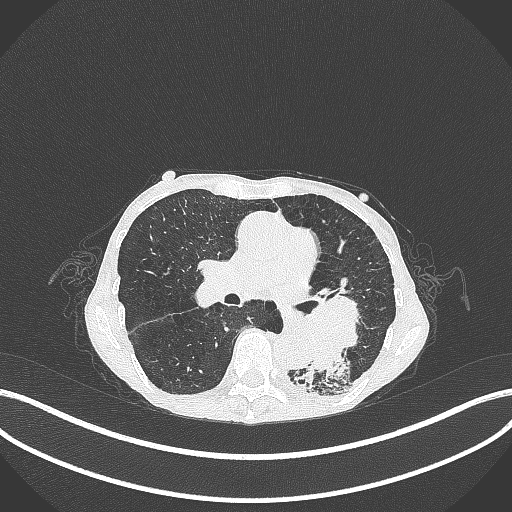
Chest CT, one axial slice; position 148 of 347 along the scan axis; reconstruction kernel B70f; 120 kVp; lung window (W 1500 / L -600 HU); 1 mm slice thickness; 512 × 512 image matrix, field of view 400 × 400 mm. Patient: female, 70 years. Case-level facts recorded for this patient, not image findings: clinical TNM (as recorded): T3 N0 M0; histopathological grade: G3.
Structures marked on this image (rectangle marked by the reading radiologist):
- lung tumour (recorded histology: small cell carcinoma): box from (x=282, y=285) to (x=365, y=379) px